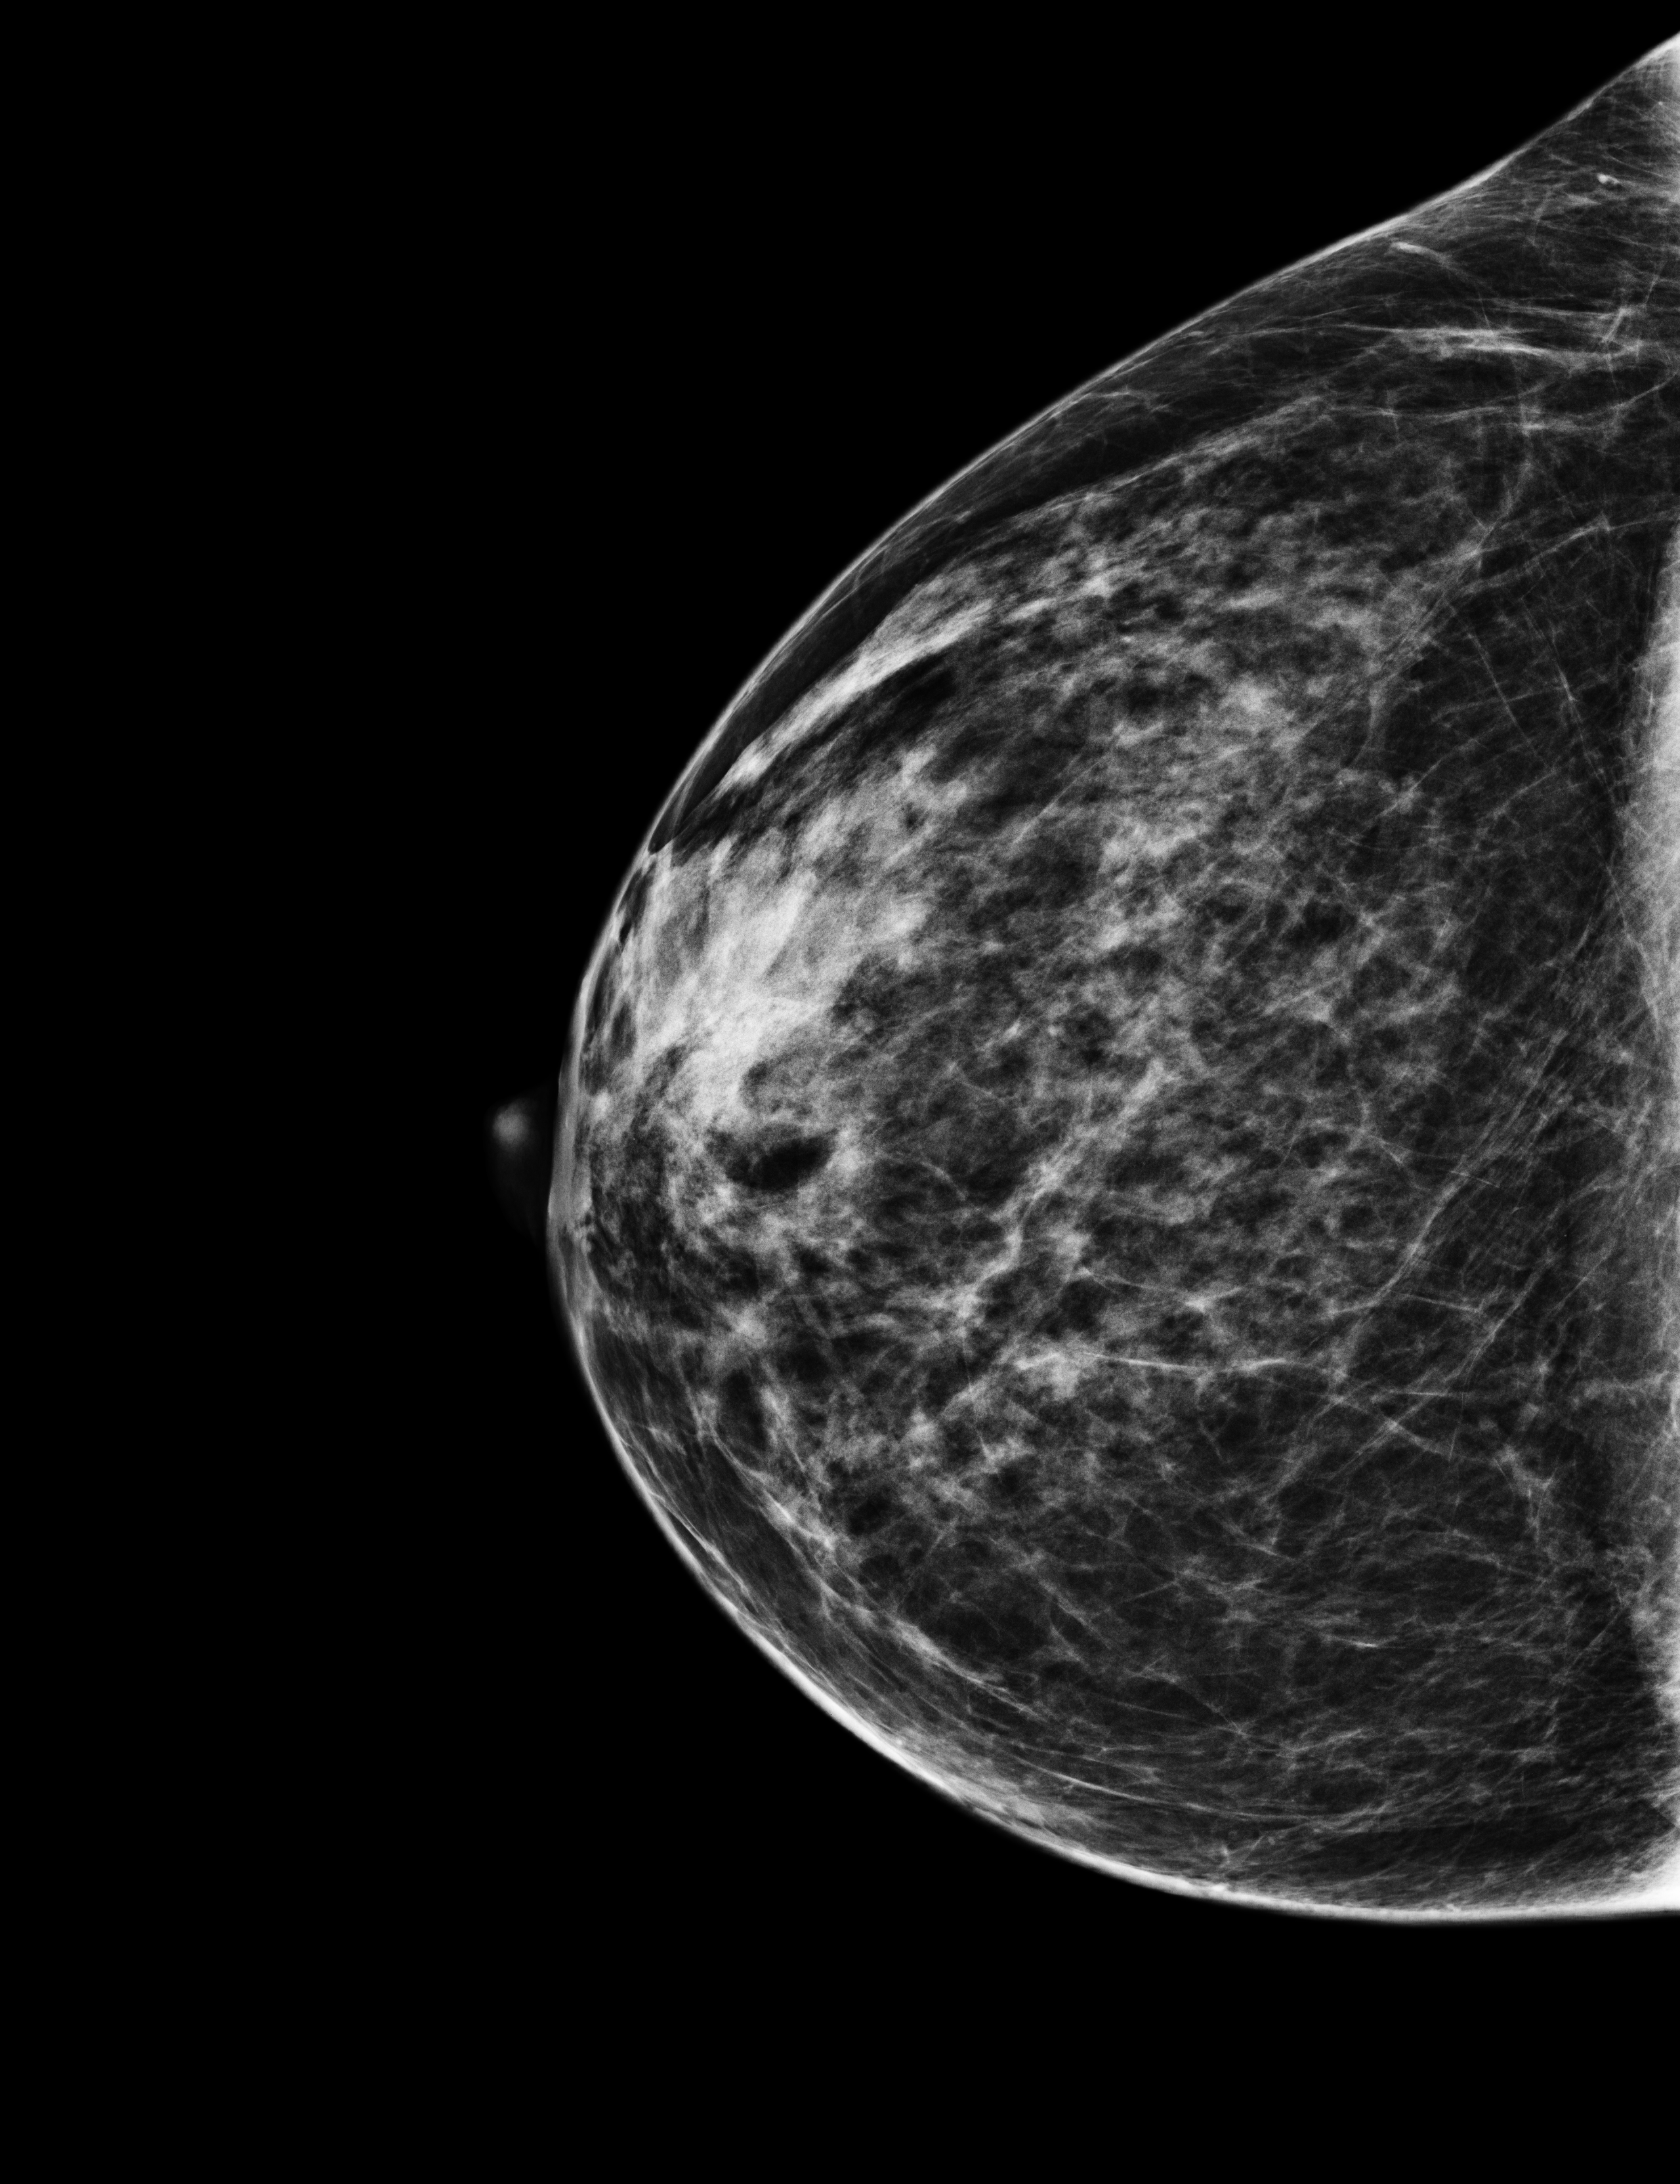
Digital mammogram (FFDM); right breast; cranio-caudal projection; annual screening mammography examination; system: Selenia Dimensions. Patient aged 50 years (female).
Breast density at the screening exam (both breasts): heterogeneously dense (BI-RADS density category c). Final BI-RADS category for the screening round (tomosynthesis exam, both breasts): category 1. Recall: no recall after this screen.